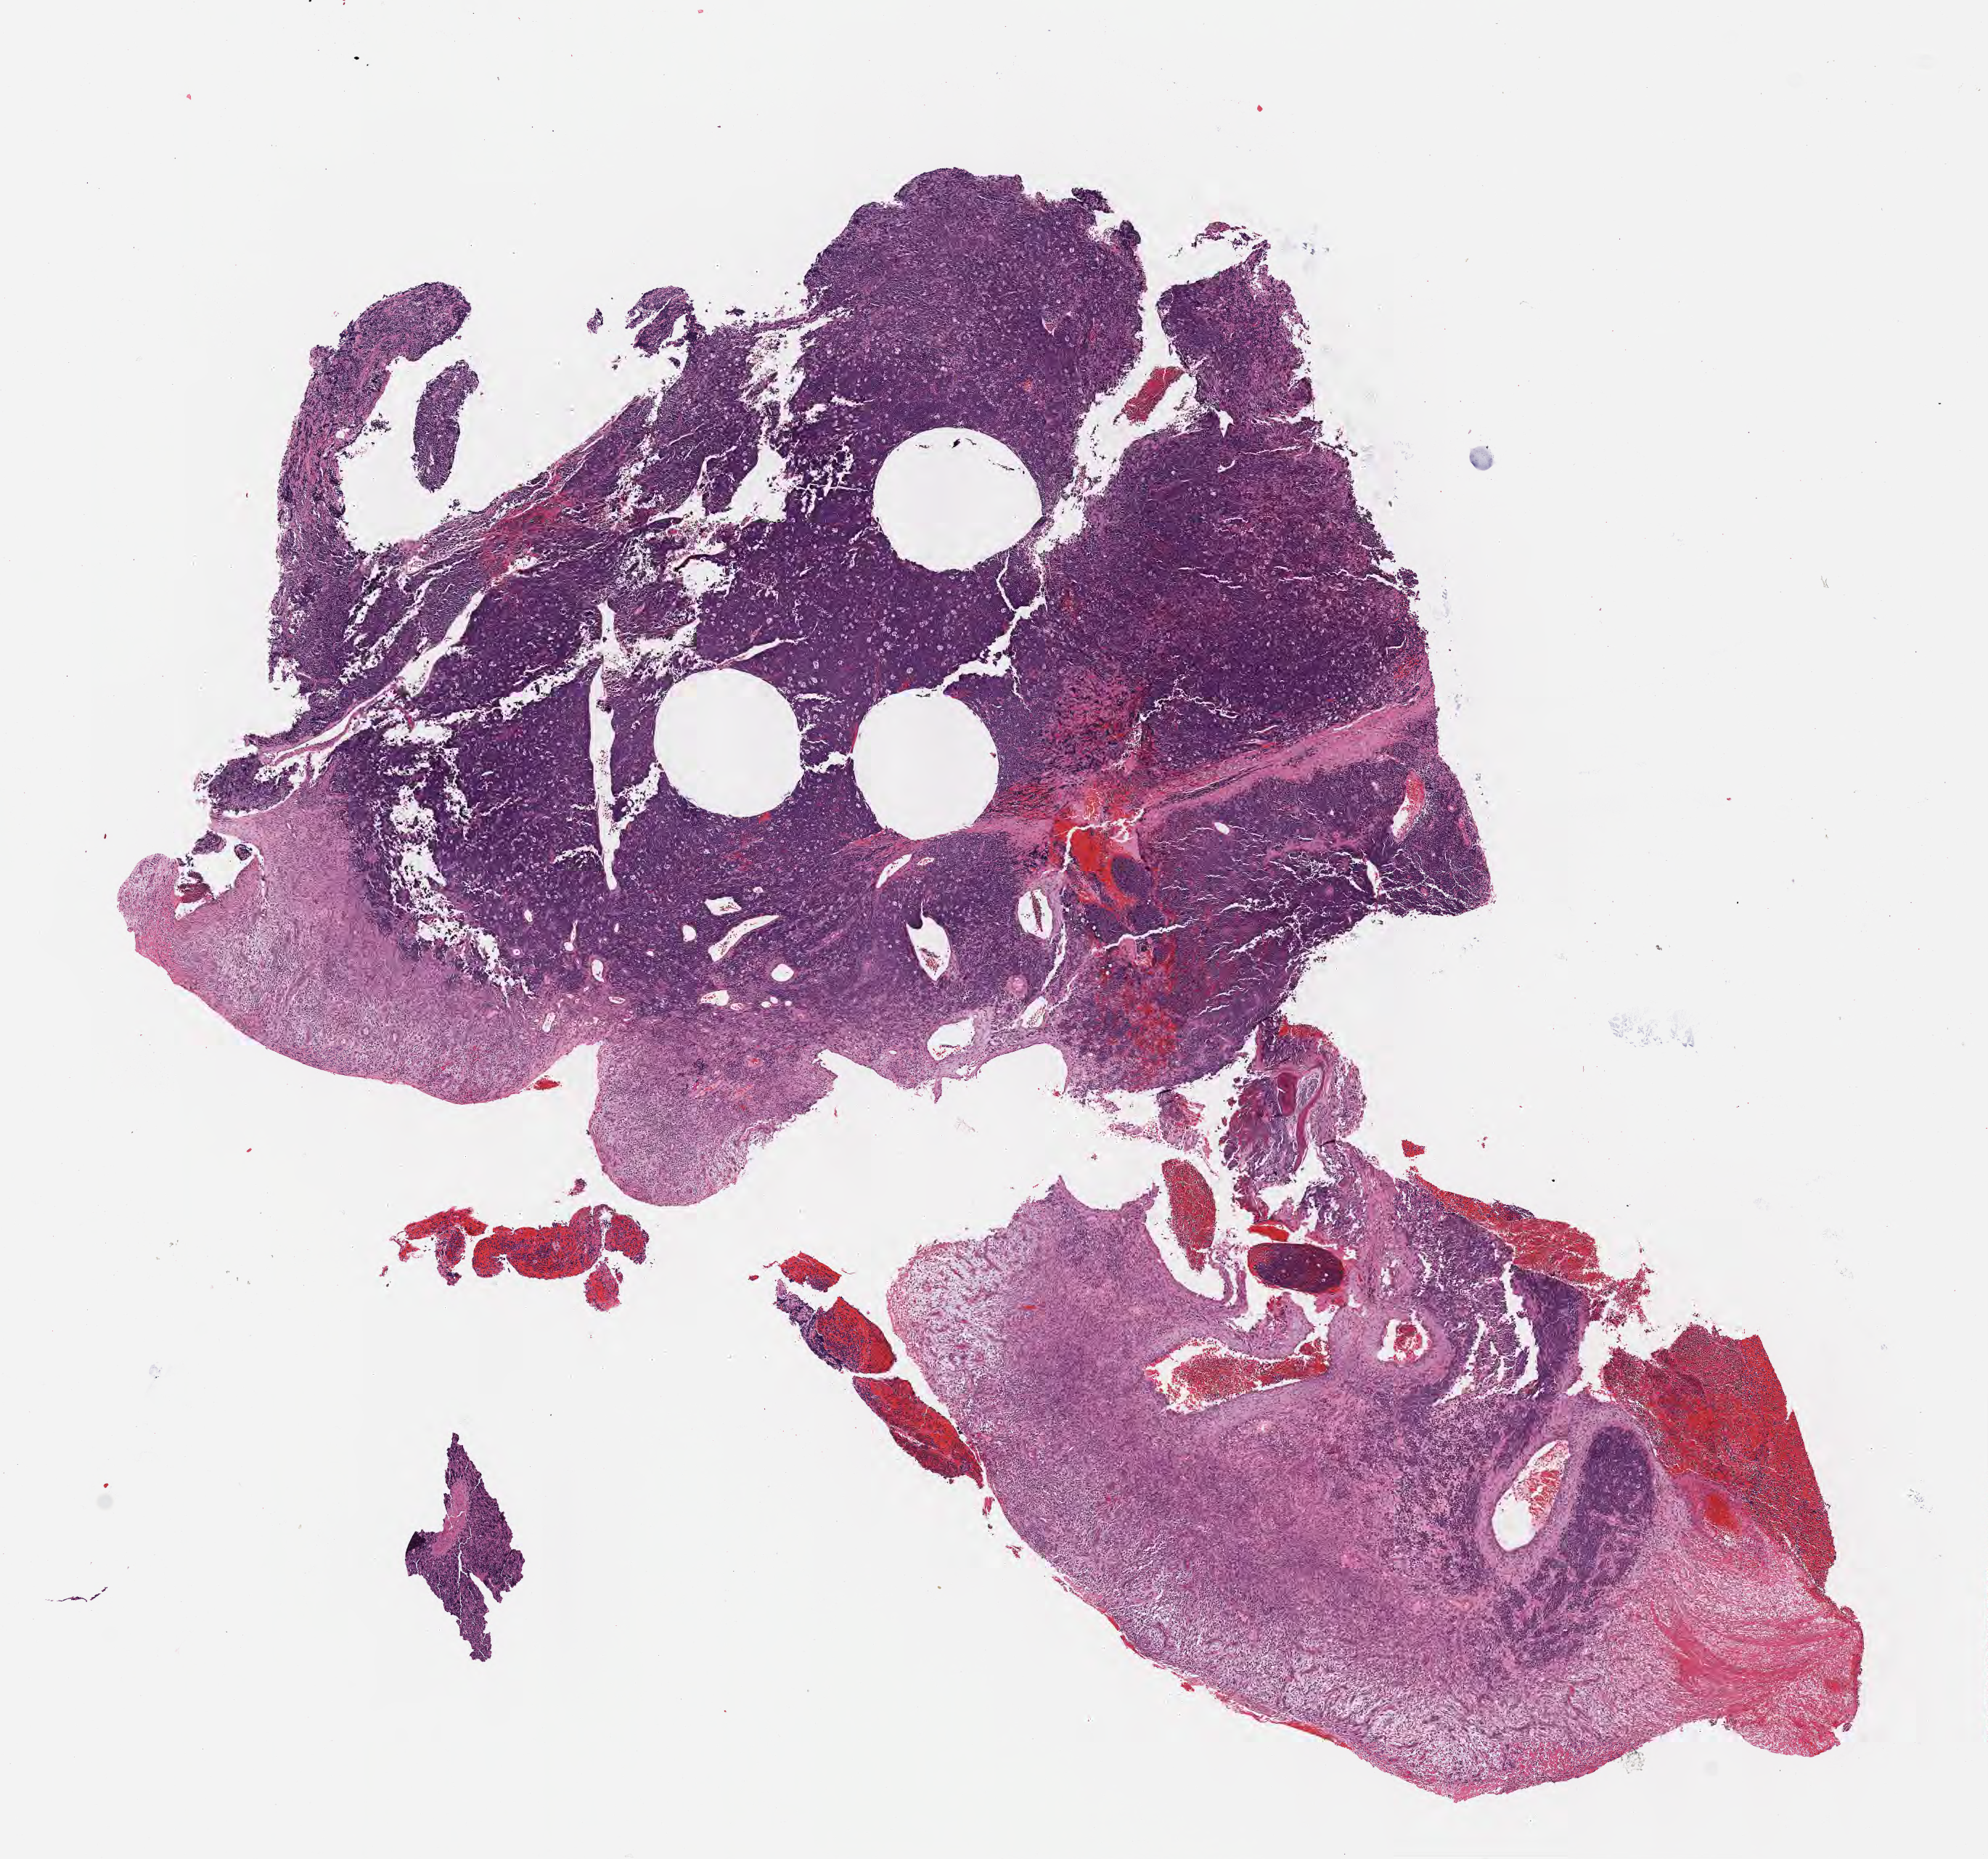
Hematoxylin and eosin (H&E) whole-slide image, shown as a low-resolution overview of the whole scanned area (about 11.1 x 10.3 mm), formalin-fixed paraffin-embedded section, specimen: primary tumor, anatomic site: mandible. Male patient; age at initial diagnosis 6 years. Pathologist review of this section (percent, as recorded): tumor cells 60%, tumor nuclei 85%, stromal cells 20%, necrosis 10%, normal cells 10%. Infiltration values recorded for this section: lymphocyte infiltration 50%, monocyte infiltration 20%, neutrophil infiltration 15%.
Diagnosis: Burkitt lymphoma, NOS. Ann Arbor stage (patient): Stage IV. Section: top of the tissue portion.